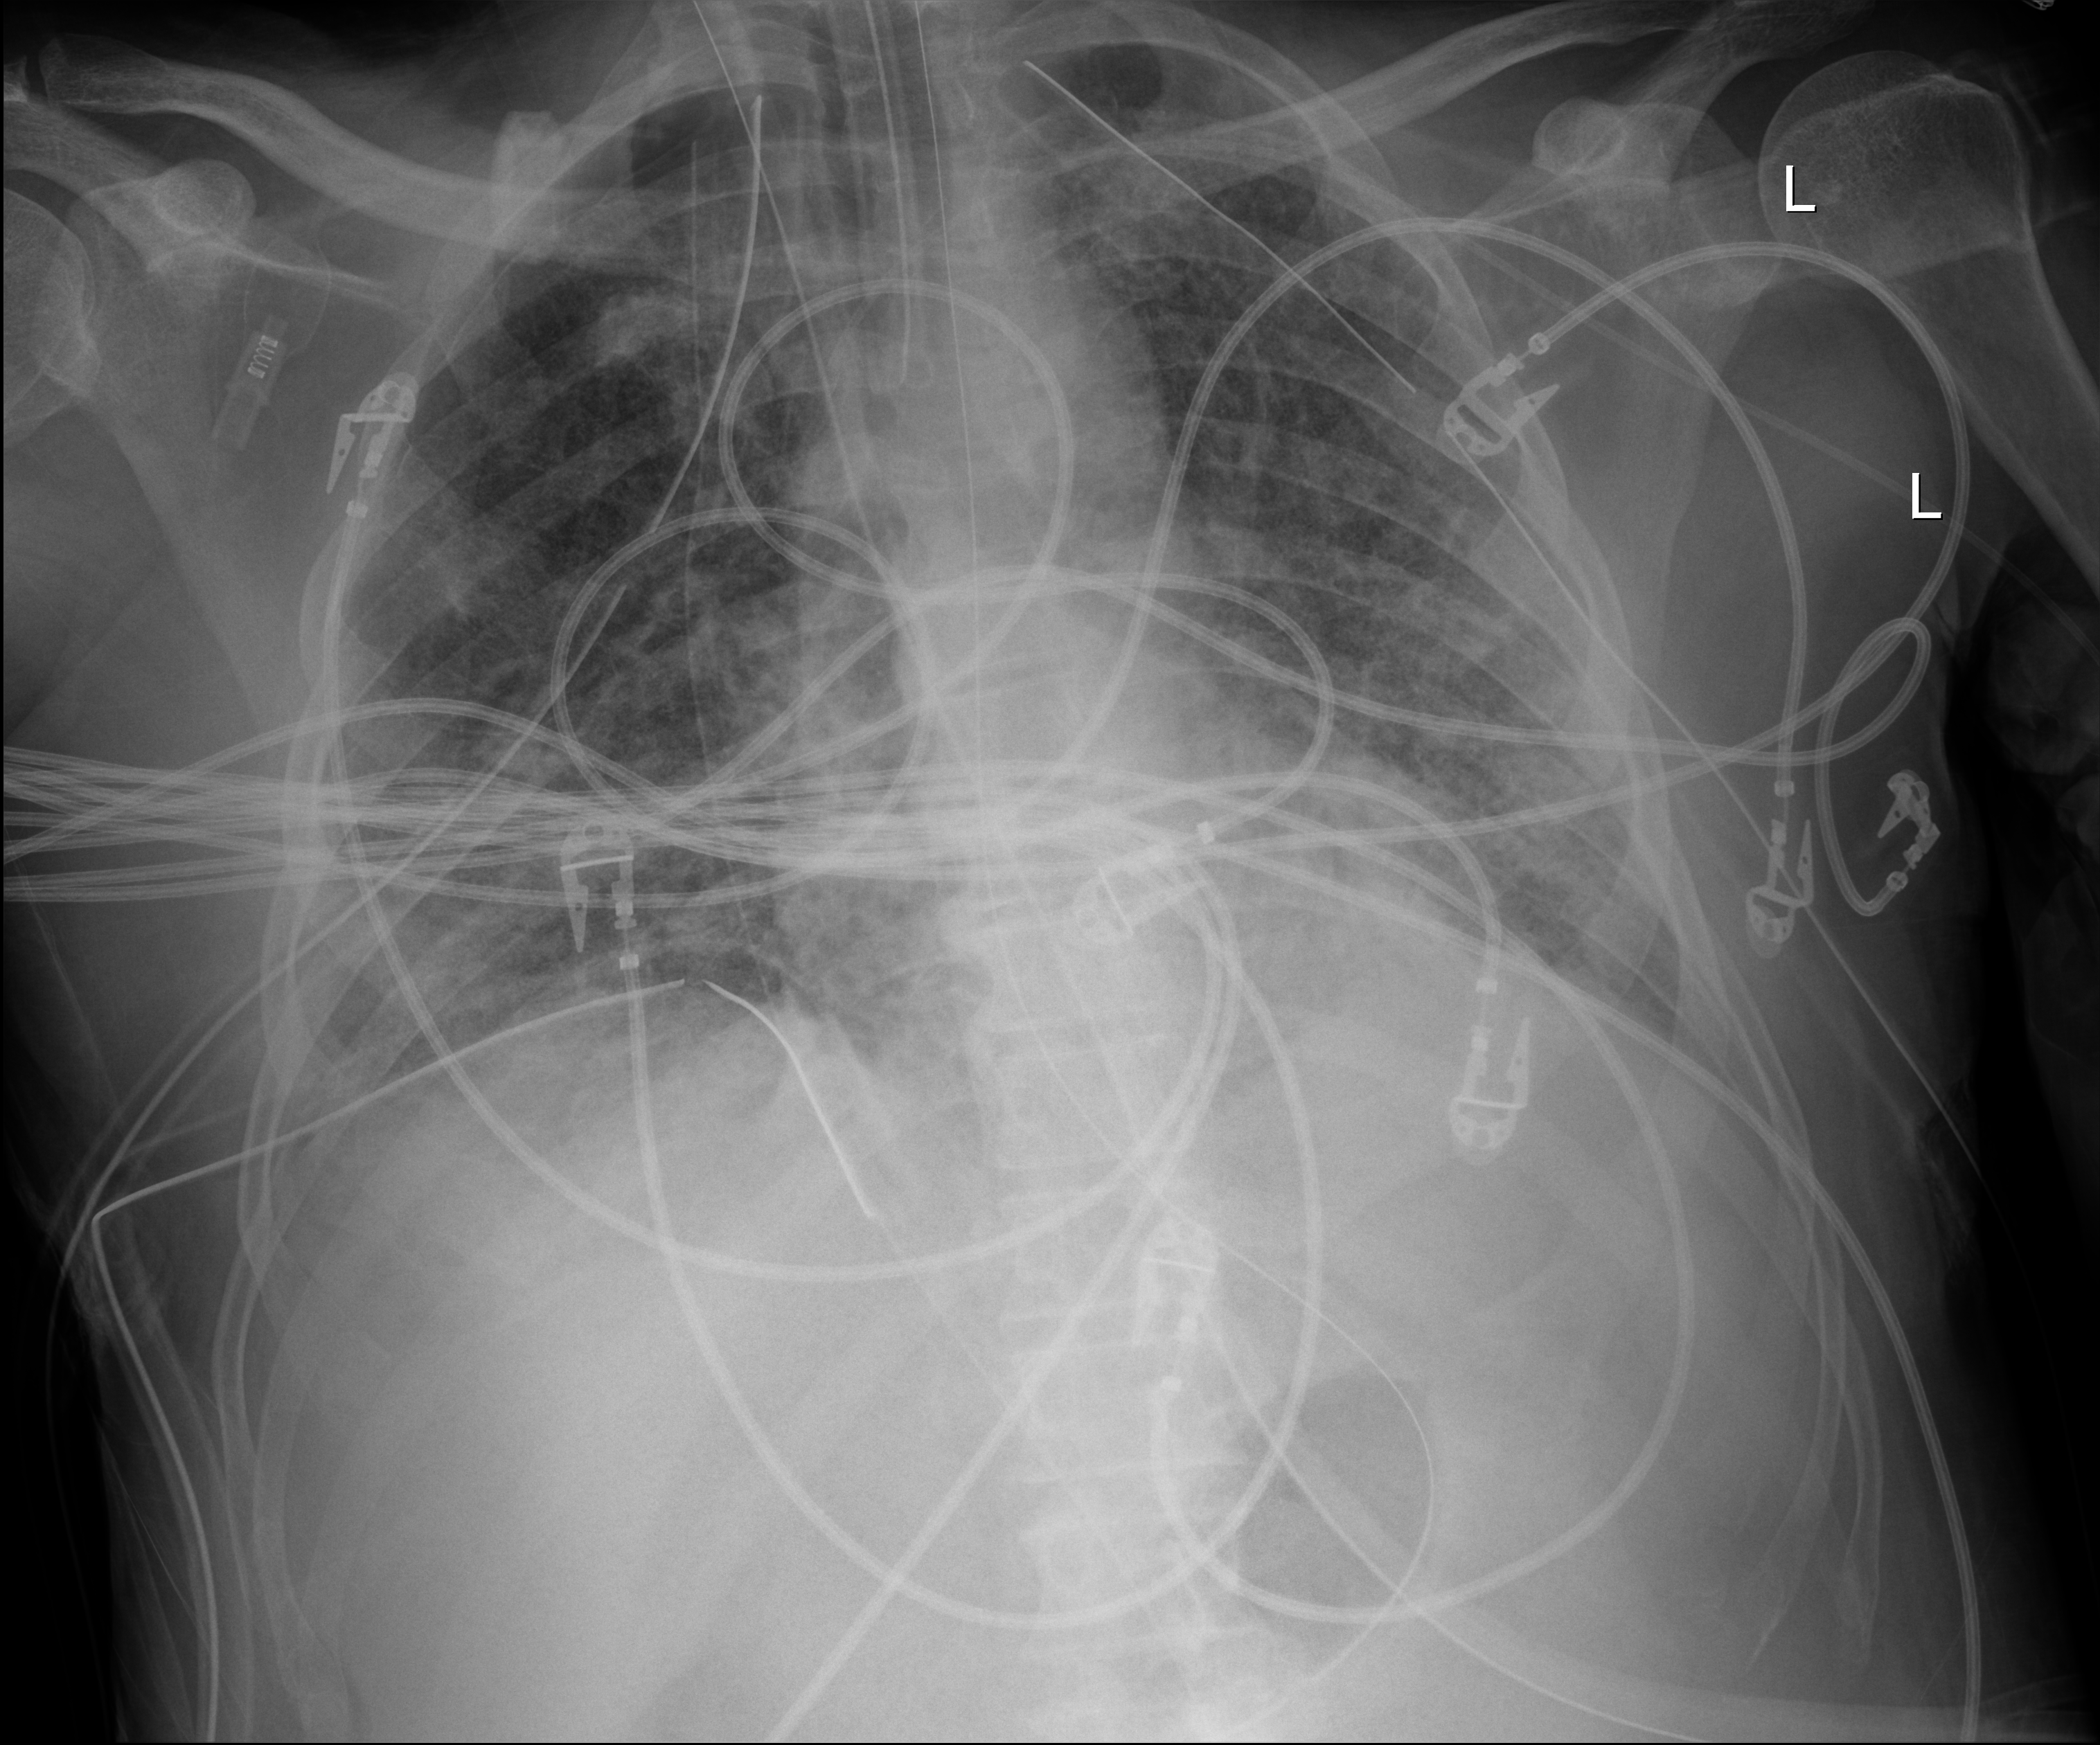
Chest X-ray (portable), anteroposterior (AP) projection. Patient hospitalised with COVID-19; male, aged 18–59 years.
Hospital-stay facts (about this admission, not read from this image; timing relative to this image not recorded): other chronic lung disease (admission record): no.